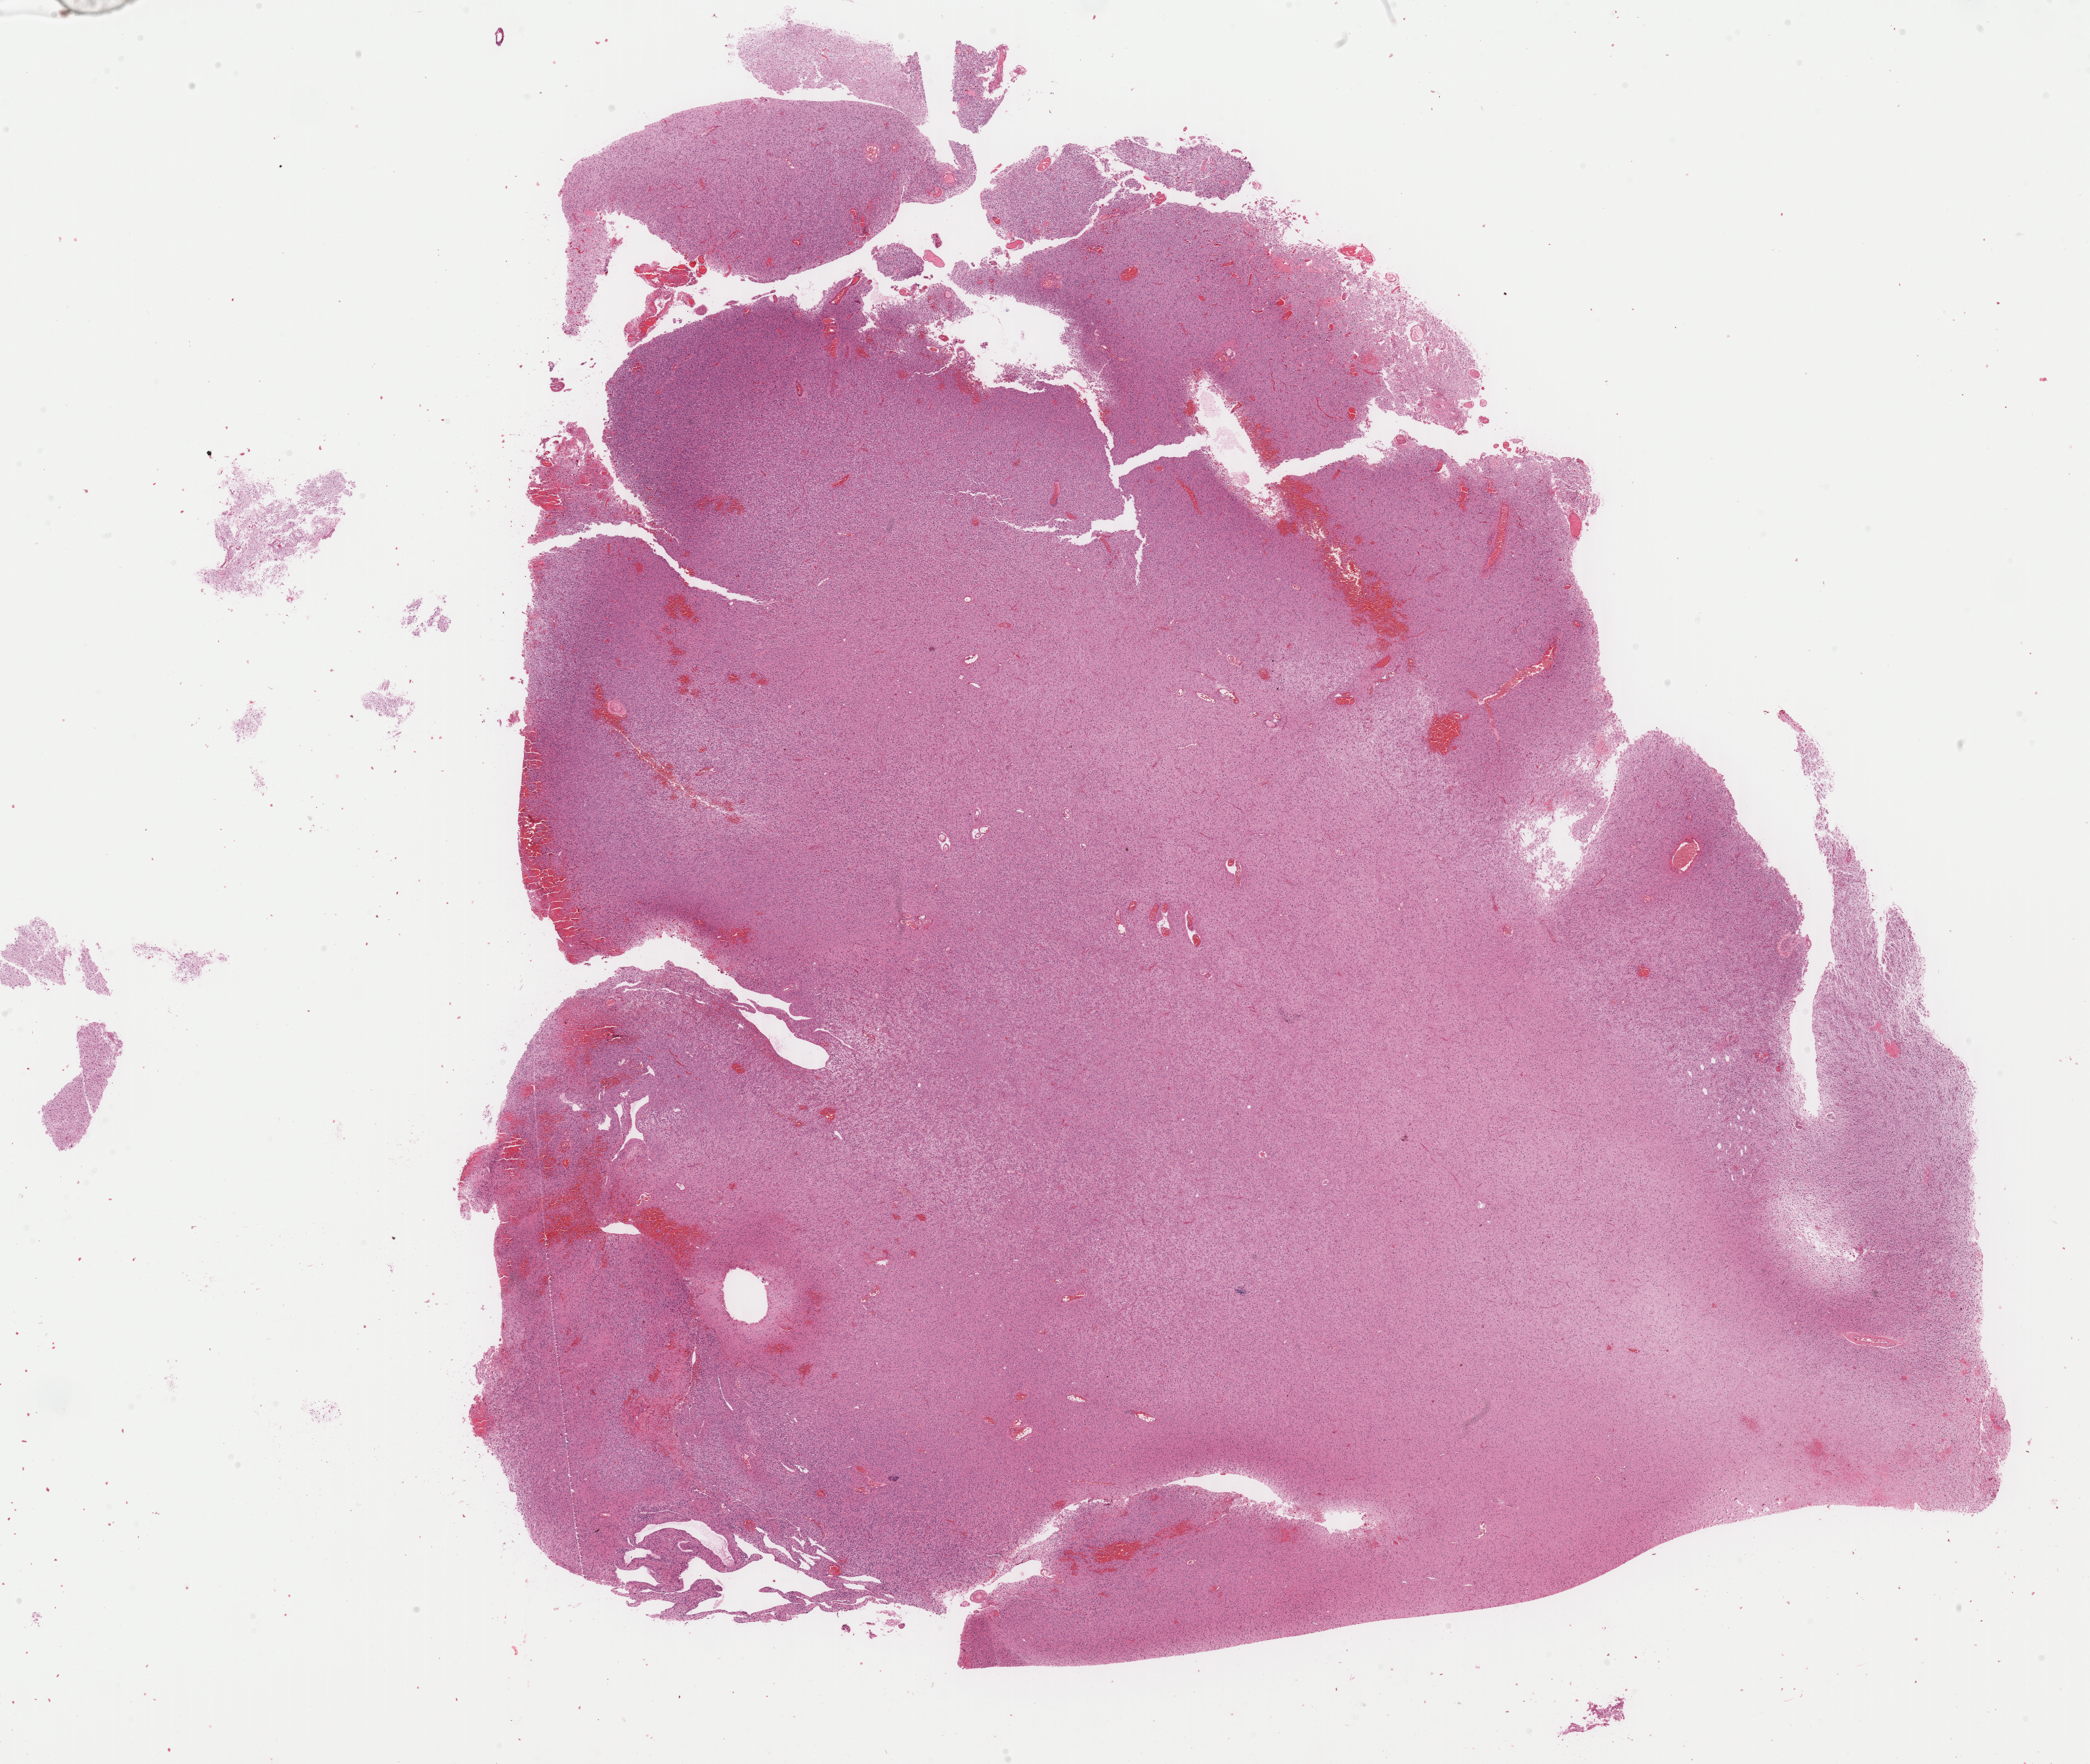
Digitized Hematoxylin and eosin (H&E) stained tissue section (whole slide) — shown as a low-resolution overview of the whole scanned area (about 25.1 x 21.2 mm), formalin-fixed paraffin-embedded (FFPE) diagnostic section, primary tumour sample from the brain. Patient: male, age at initial diagnosis 32 years. Histologic grade: G3 (poorly differentiated).
- laterality: left
- pathologic diagnosis: Mixed glioma (cerebrum)